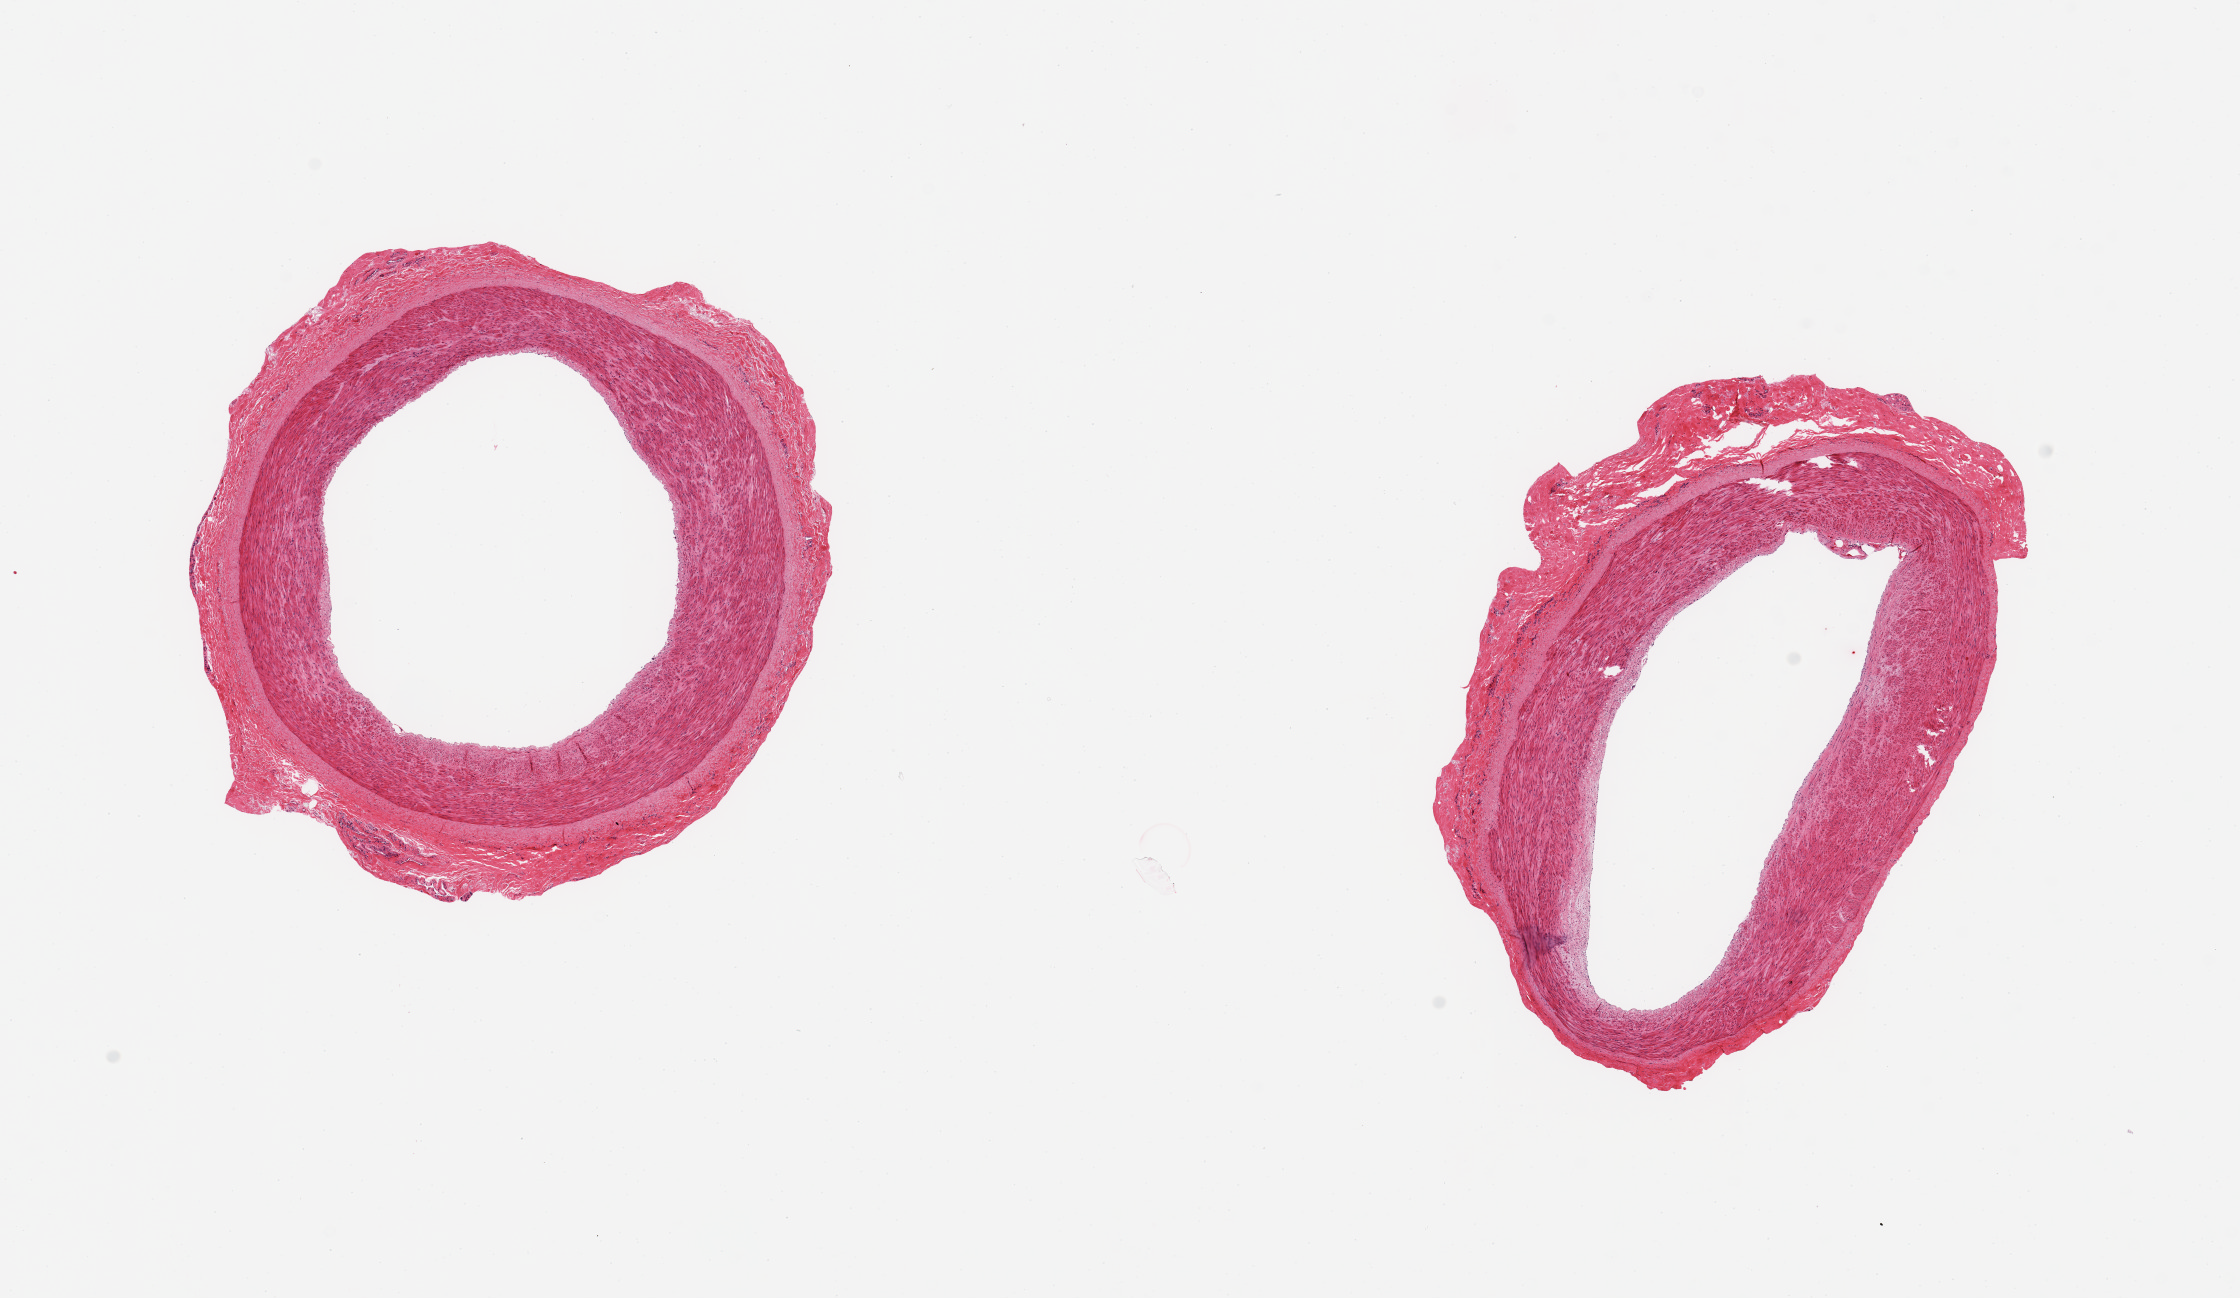
Digitized hematoxylin and eosin (H&E)-stained section, brightfield, a low-resolution overview of the entire scanned area, about 17.7 x 10.3 mm, PAXgene-fixed, paraffin-embedded tissue, section of tibial artery (target tissue), donor tissue sample. Donor sex: male.
* reviewer comment on this tissue sample: 2 pieces; well trimmed; minimal intimal thickening